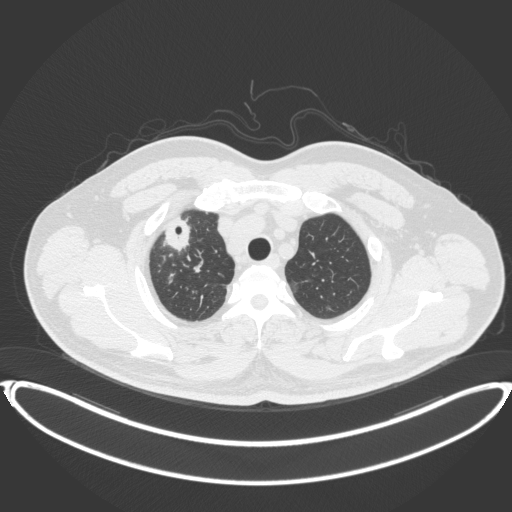
Chest CT, one axial slice. Position 332 of 399 along the scan axis. Reconstruction kernel B31f. 120 kVp. Lung window (W 1500 / L -600 HU). 1 mm slice thickness. 512 × 512 image matrix, field of view 445 × 445 mm. Male patient, age 53 years. Case-level facts recorded for this patient, not image findings: clinical TNM (as recorded): T2a N0 M0.
Structures marked on this image (rectangle marked by the reading radiologist):
- lung tumour (recorded histology: adenocarcinoma): bounding box [x1, y1, x2, y2] px = [160, 215, 200, 255]